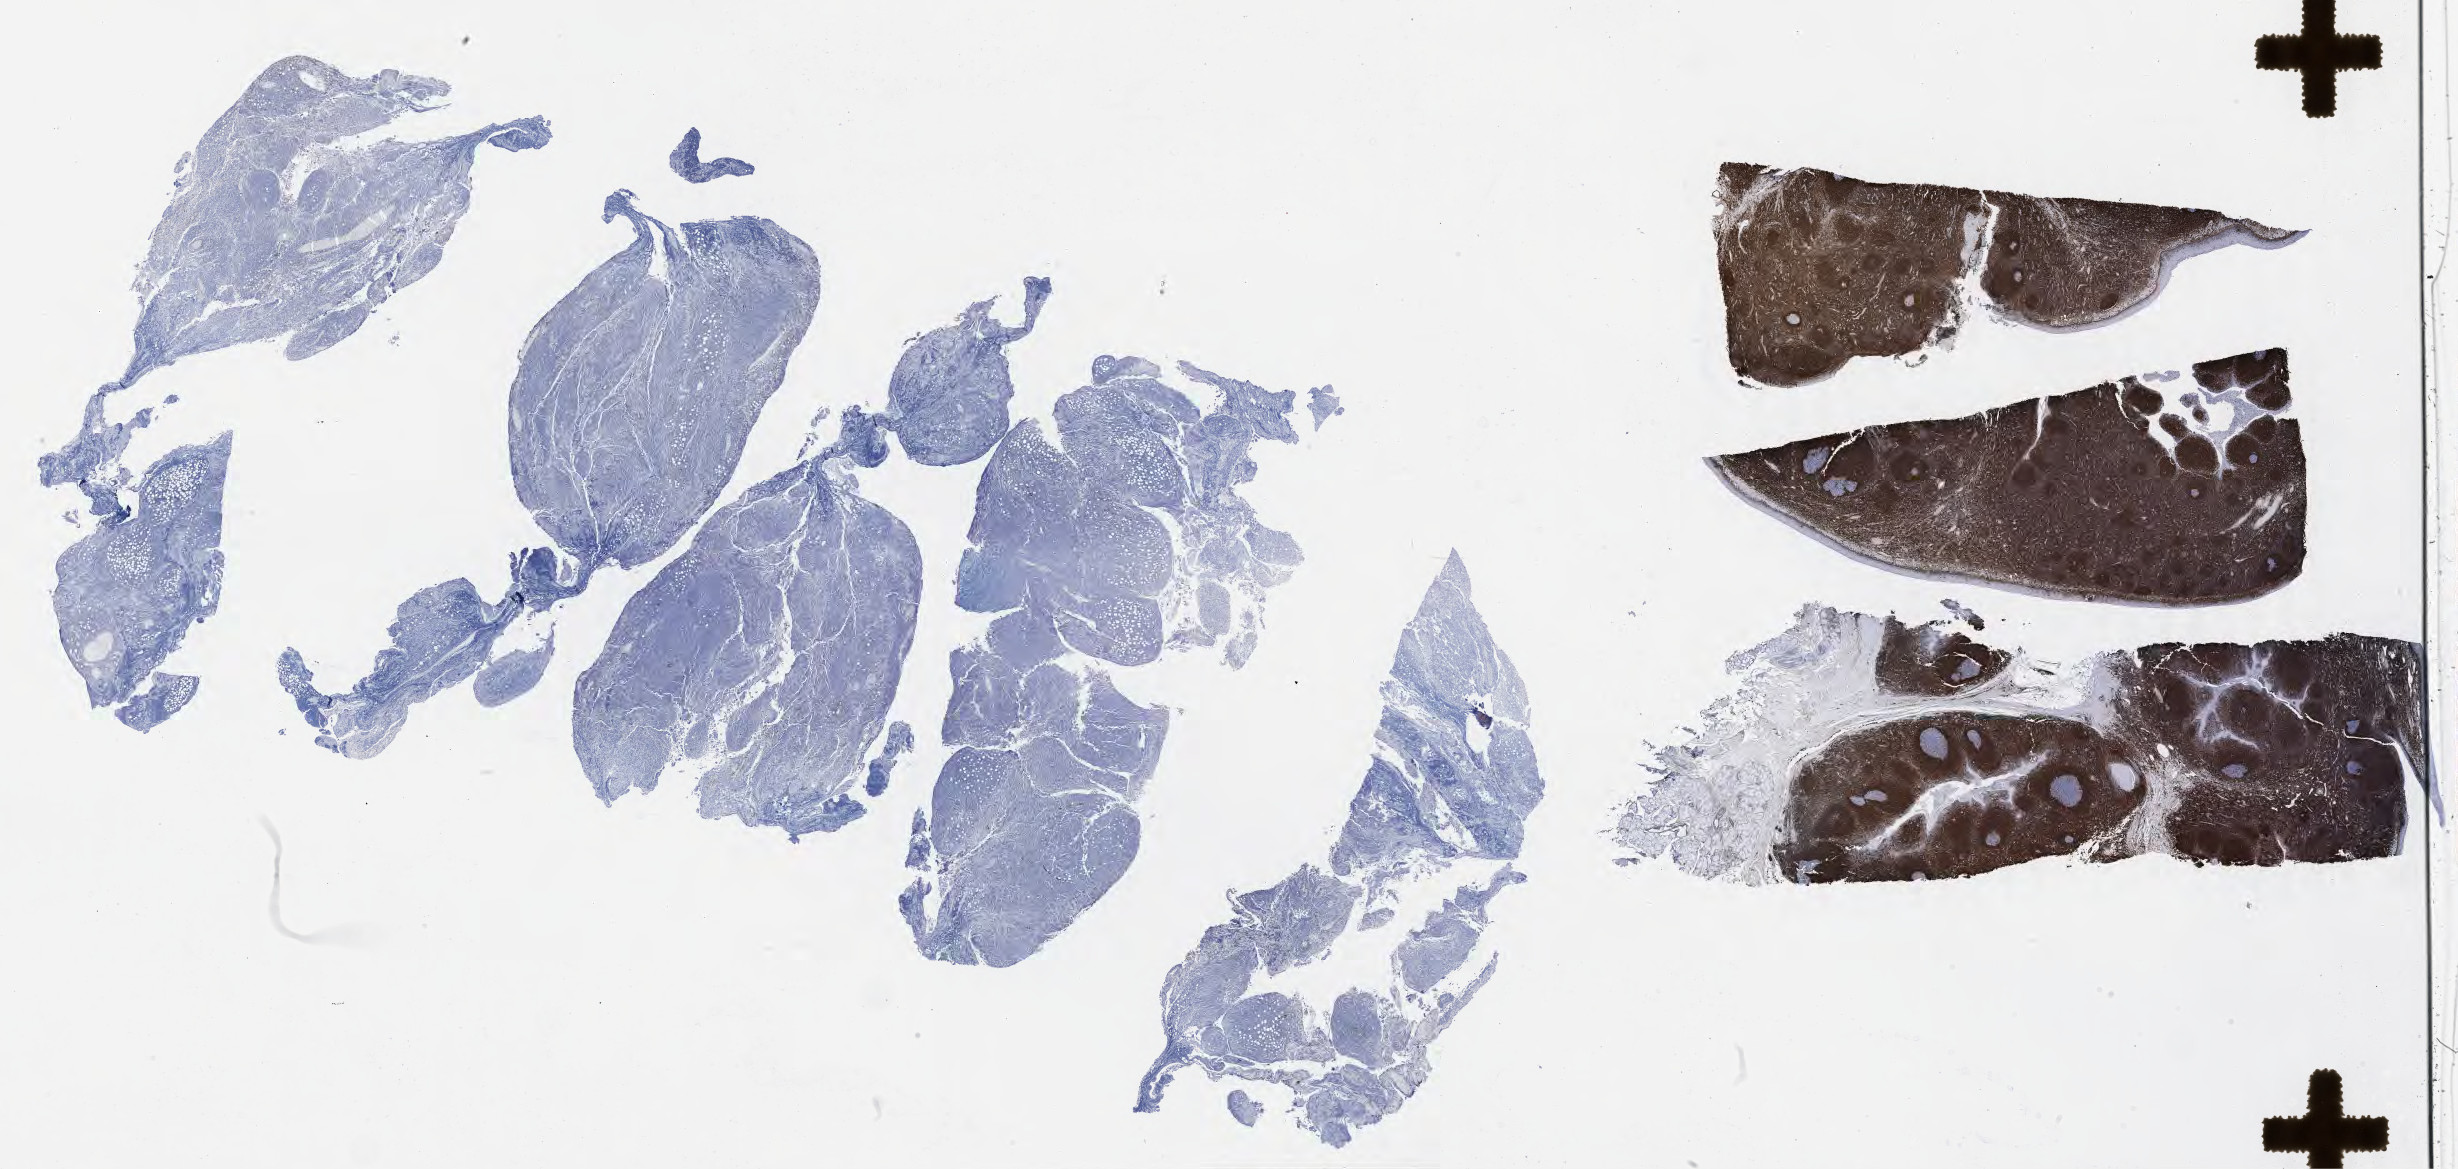
Immunohistochemistry (IHC) whole-slide image stained for BCL2 — shown as a low-resolution overview of the whole scanned area (about 39.7 x 18.9 mm), specimen: tumor tissue, anatomic site: peritoneum. Male, age 8 years at initial diagnosis.
Histologic diagnosis: Burkitt lymphoma, NOS.